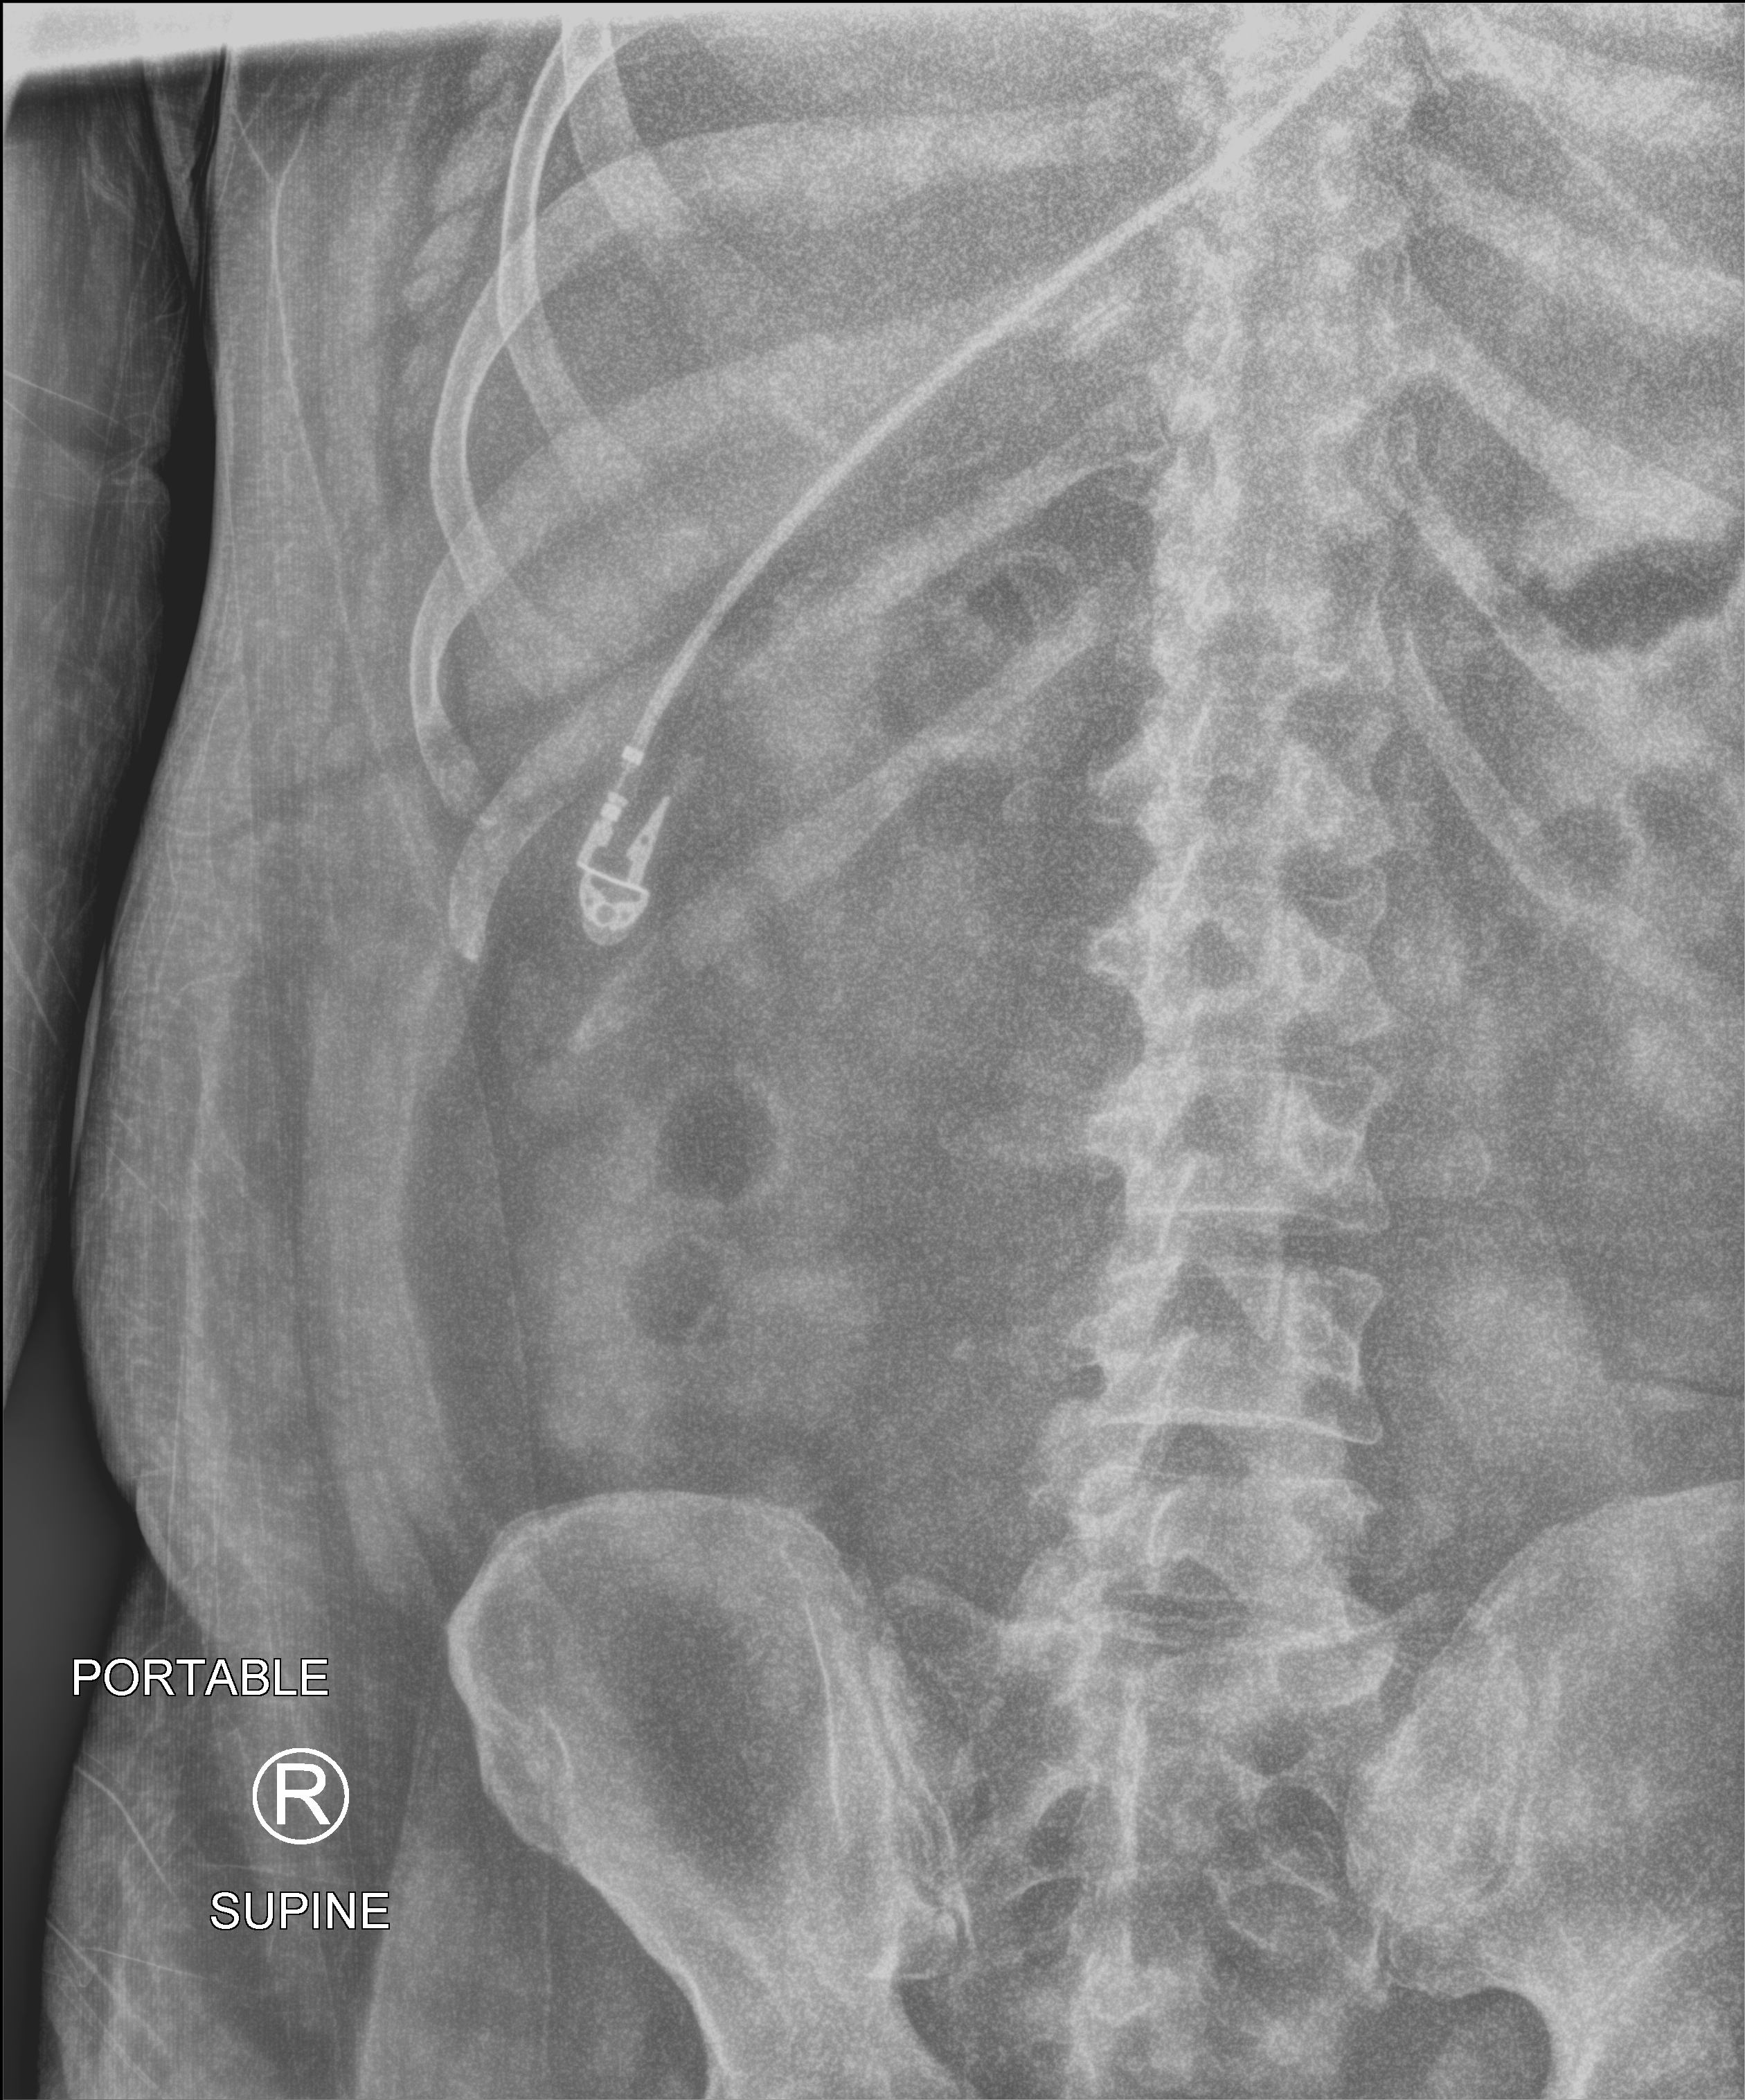
Bedside abdomen radiograph (computed radiography), anteroposterior (AP) projection. Male patient hospitalised with COVID-19, age 18–59 years.
From the hospital-stay record, not from the radiograph (when in the stay this image was taken is not recorded): mechanically ventilated during this hospital stay: yes.